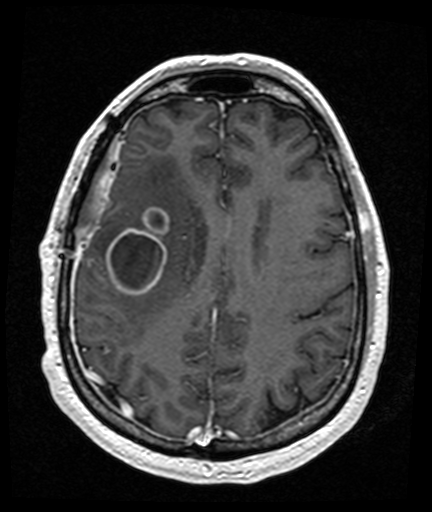
Brain MRI from a brain-tumour surgery series, one axial slice; position 56 of 176 along the scan axis; T1-weighted post-contrast; 1 mm slice thickness; 432 × 512 image matrix. From the clinical record (not read from this slice): histopathology: Glioblastoma; WHO grade: 4; IDH mutation: no; tumour location: Right Frontal Temporal, Posterior Sylvian Fissure.
Outlined on this slice (outlined manually by an expert reader):
- tumour: bounding box (x1, y1, x2, y2) in pixels: (107, 208, 169, 296)